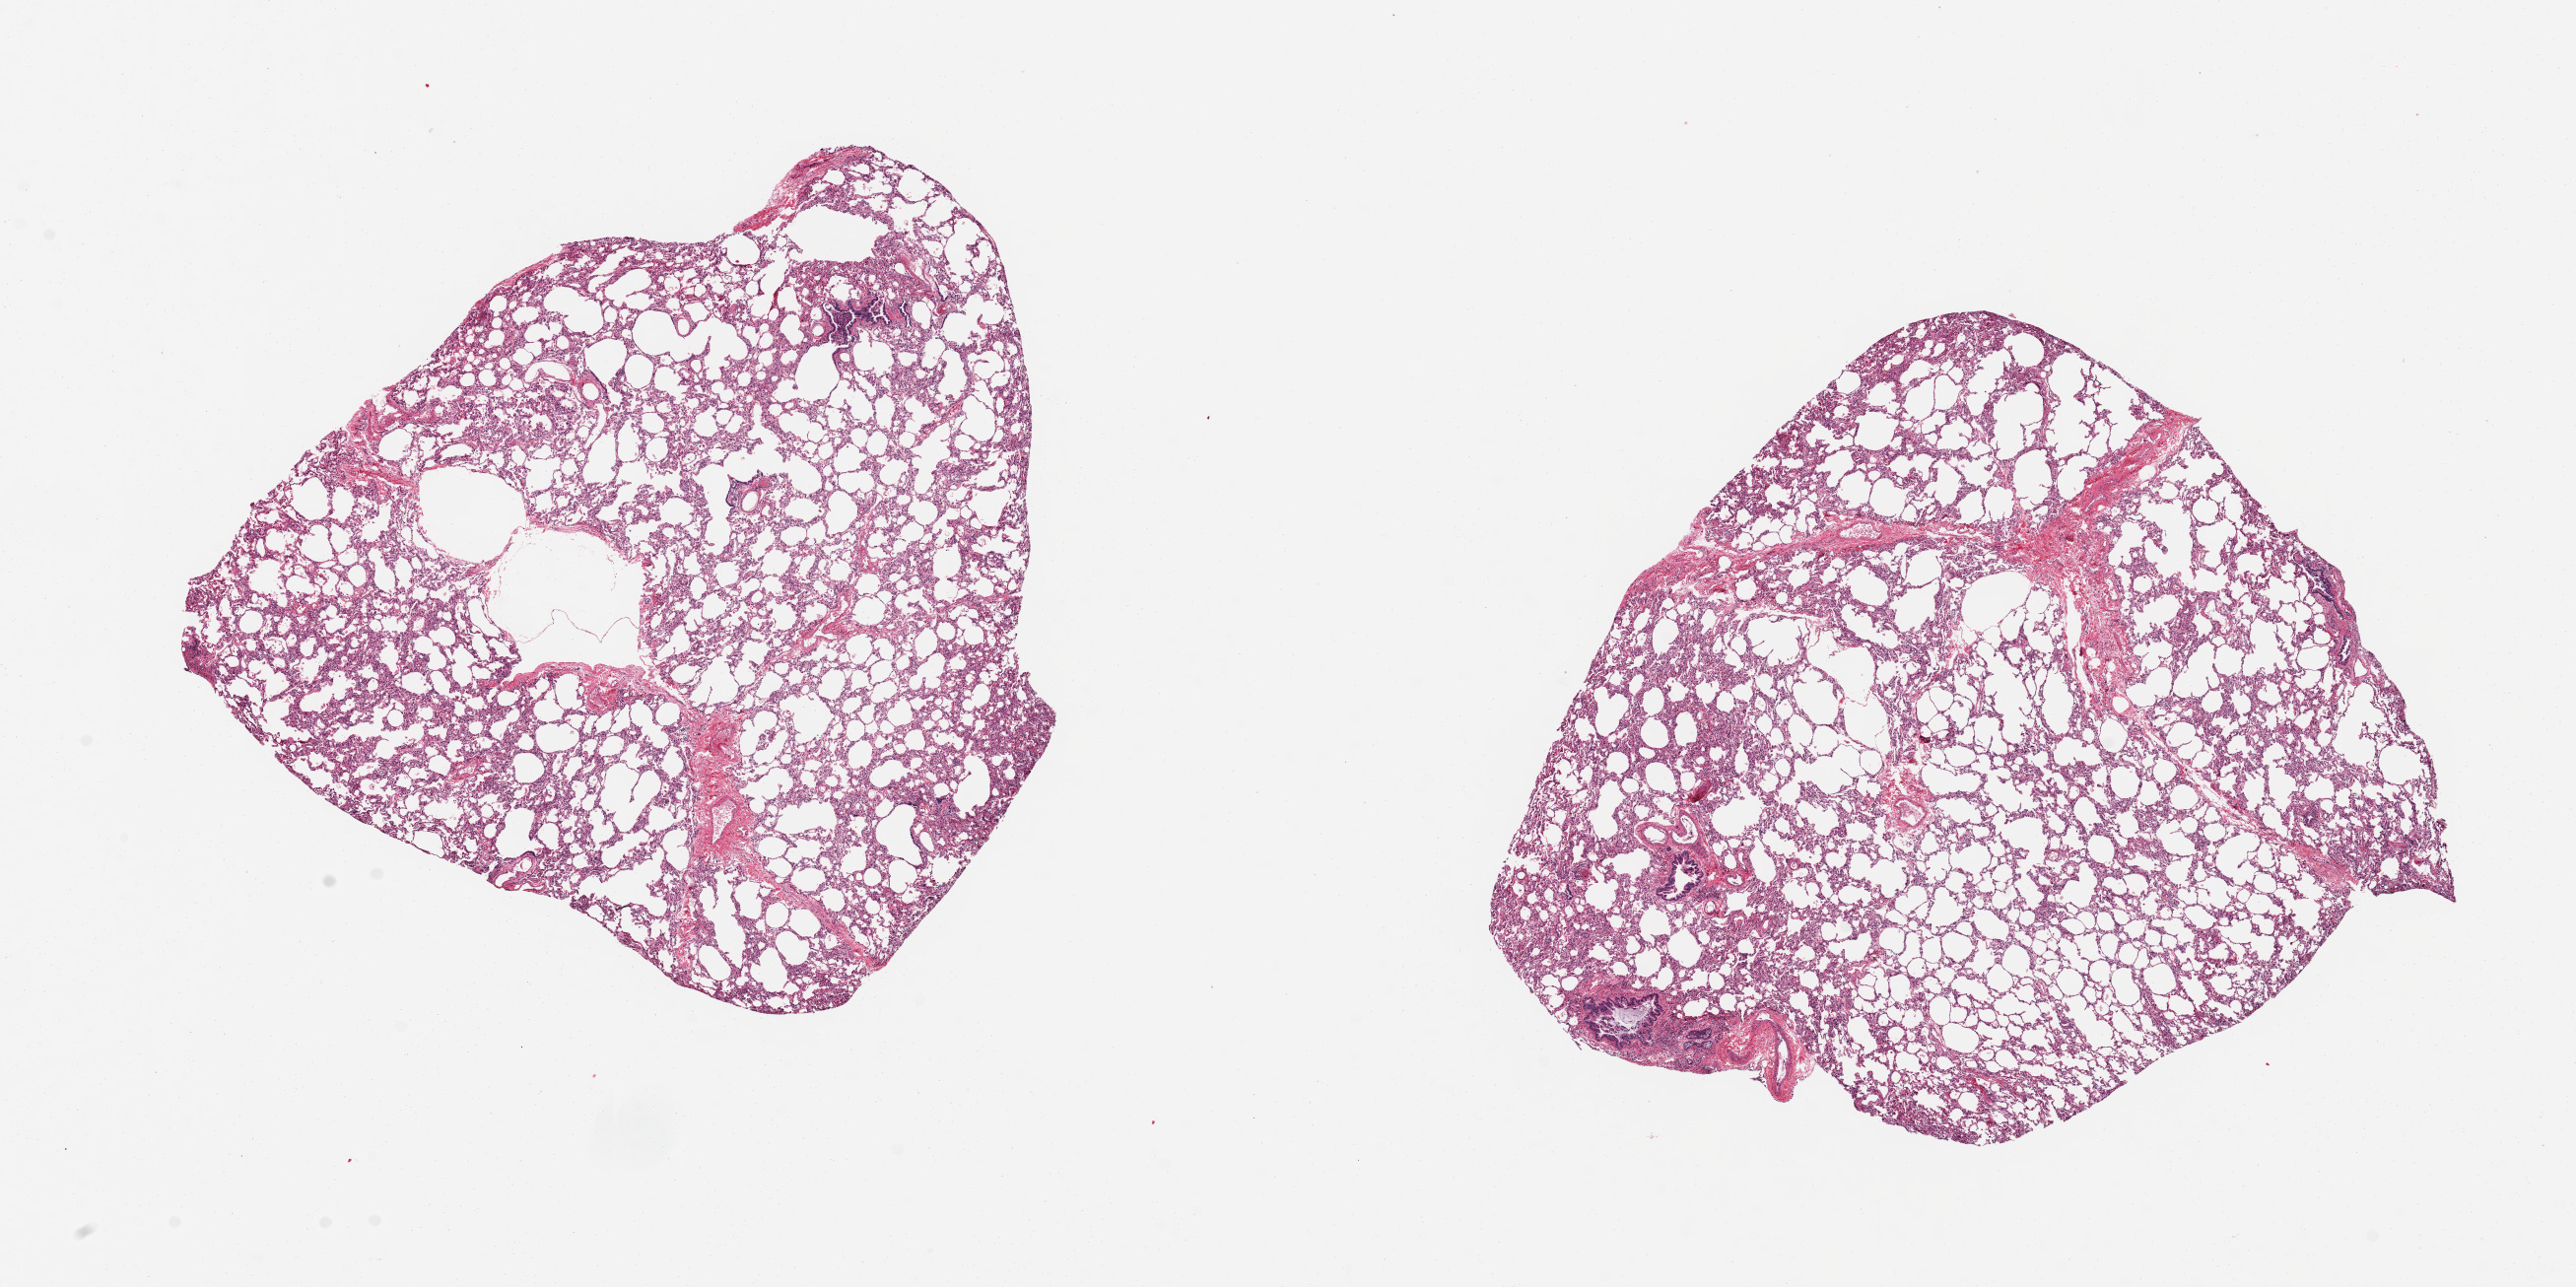
Digitized H&E-stained section, whole scanned area (about 20.7 x 10.3 mm) shown as a low-resolution overview; PAXgene-fixed, paraffin-embedded tissue; section of lung (target tissue); tissue donor sample.
Pathologist's review note for this sample: 2 pieces, 8x6 & 6x6; several dilated air spaces.